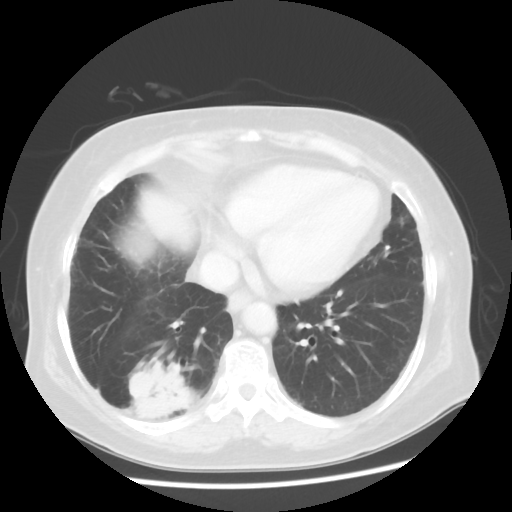
Chest CT, one axial slice. Position 19 of 56 along the scan axis. Reconstruction kernel STANDARD. 120 kVp. Lung window (W 1500 / L -600 HU). 5 mm slice thickness. 512 × 512 image matrix, field of view 360 × 360 mm. Female patient, age 64 years. From the clinical record (not read from this slice): clinical TNM (as recorded): Tis N0 M0.
Annotated regions visible in this slice (rectangle marked by the reading radiologist):
- lung tumour (recorded histology: adenocarcinoma): bounding box <122,357,195,428> (left, top, right, bottom; pixels)